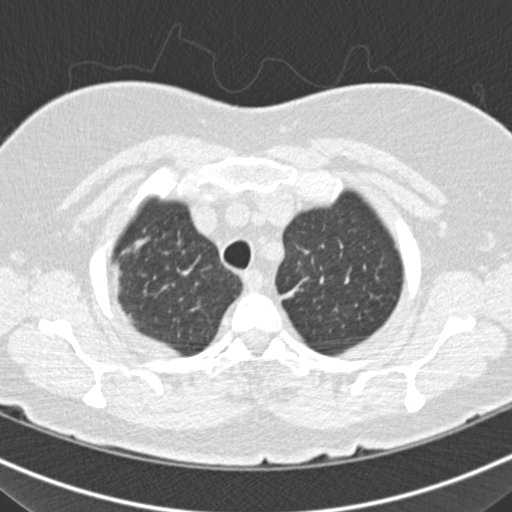
Low-dose screening chest CT, one axial slice; slice 142 of 160 in the series (ordered by position); reconstruction kernel B30f; 120 kVp; lung window (W 1500 / L -600 HU); 2 mm slice thickness; 512 × 512 image matrix.
Structures marked on this image (manually delineated by an expert):
- lesion 3 (nodule, upper lobe of right lung): bounding box <127,237,147,253> (left, top, right, bottom; pixels)